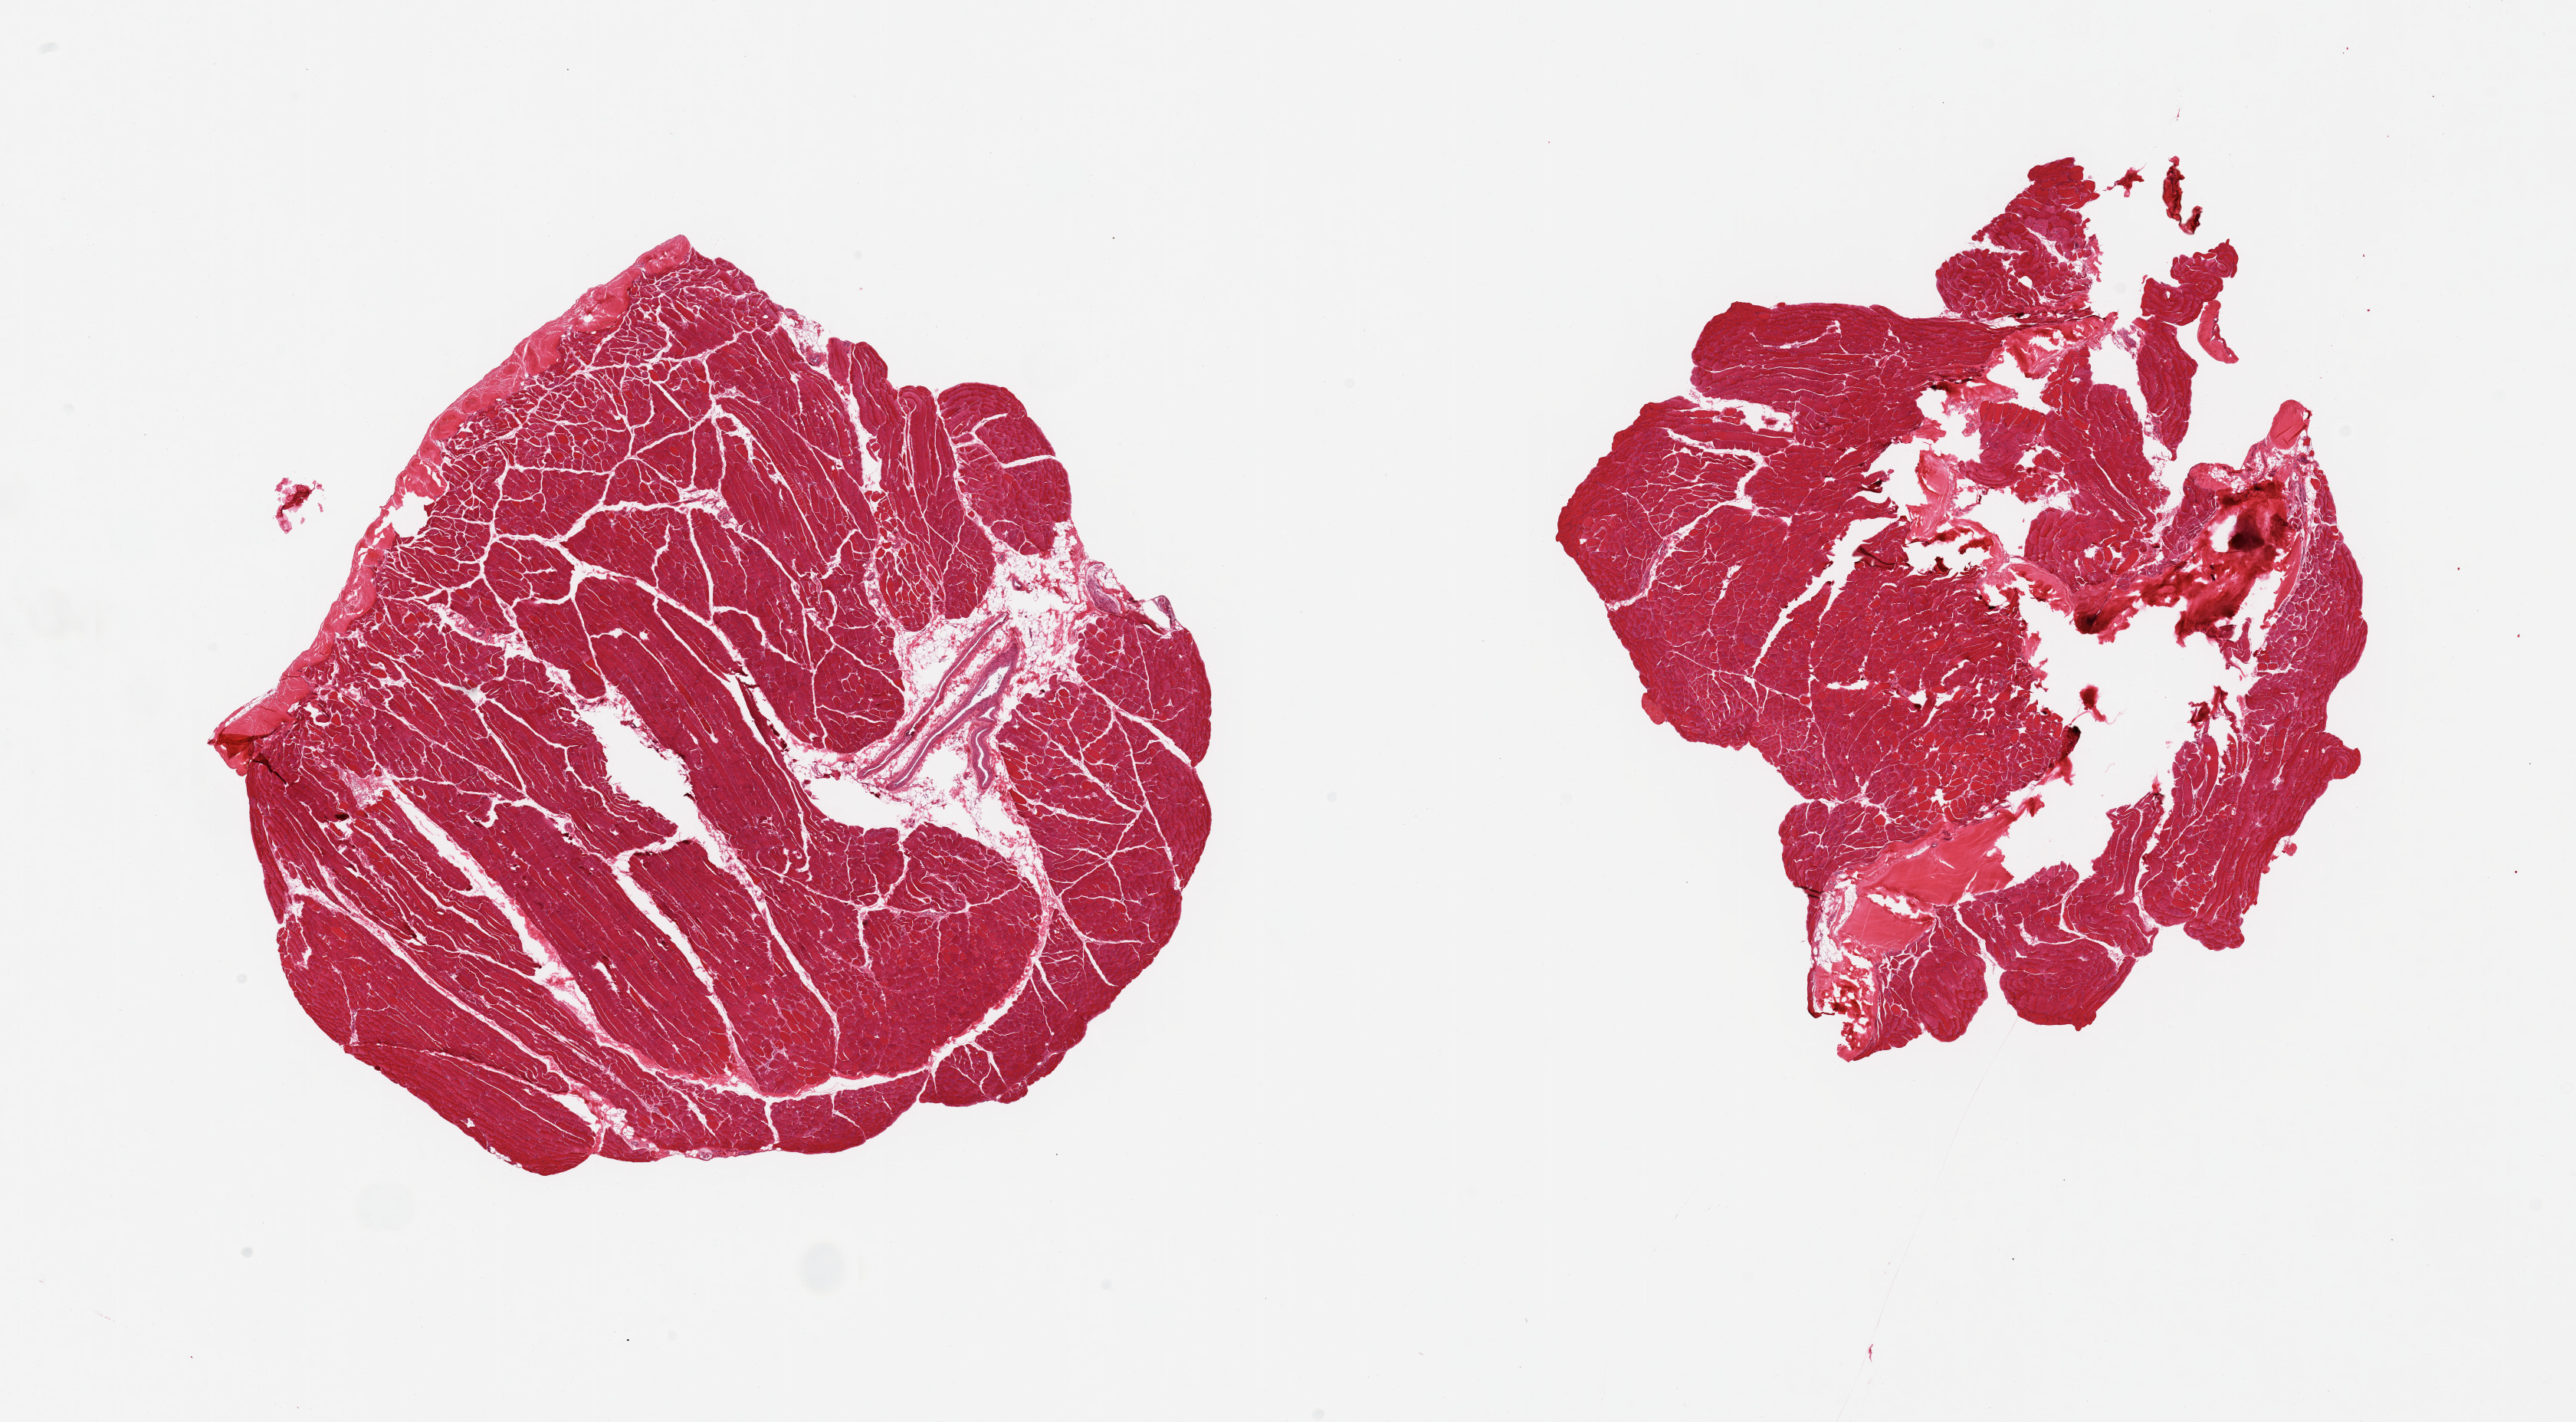
Haematoxylin and eosin whole-slide image — whole scanned area (about 26.6 x 14.7 mm) shown as a low-resolution overview, PAXgene-fixed, paraffin-embedded tissue, sampled site (target tissue): skeletal muscle, tissue donor sample. Donor sex: female.
Reviewer comment on this tissue sample: 2 pieces; 10% internal fat in one; 10% fragmented tendon in other.